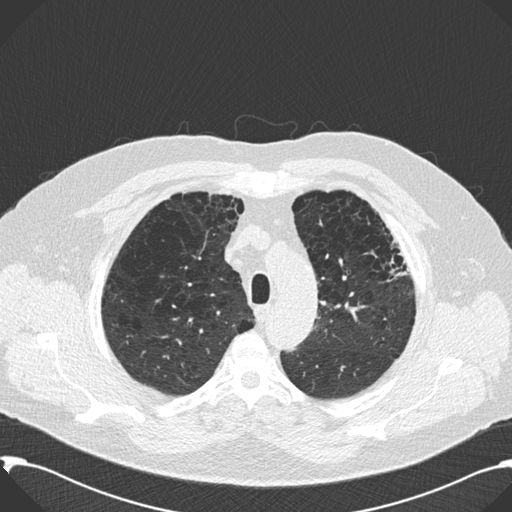
Low-dose screening chest CT, axial slice; second screening round (one year after baseline); lung window (W 1500 / L -600 HU); standard (soft-tissue) reconstruction kernel (B30f); 120 kVp; 512 × 512 image matrix. Male participant, aged 59 years at enrolment.
Expert-annotated lung lesion, bounding box [x1, y1, x2, y2] px = [365, 227, 416, 301]. Screening reader's record for this exam: no non-calcified nodule ≥4 mm recorded. Participant outcome: lung cancer diagnosed 518 days after this screen — bronchiolo-alveolar carcinoma, mixed mucinous and non-mucinous, left upper lobe, stage IA (AJCC 6th edition), 20 mm at pathology.